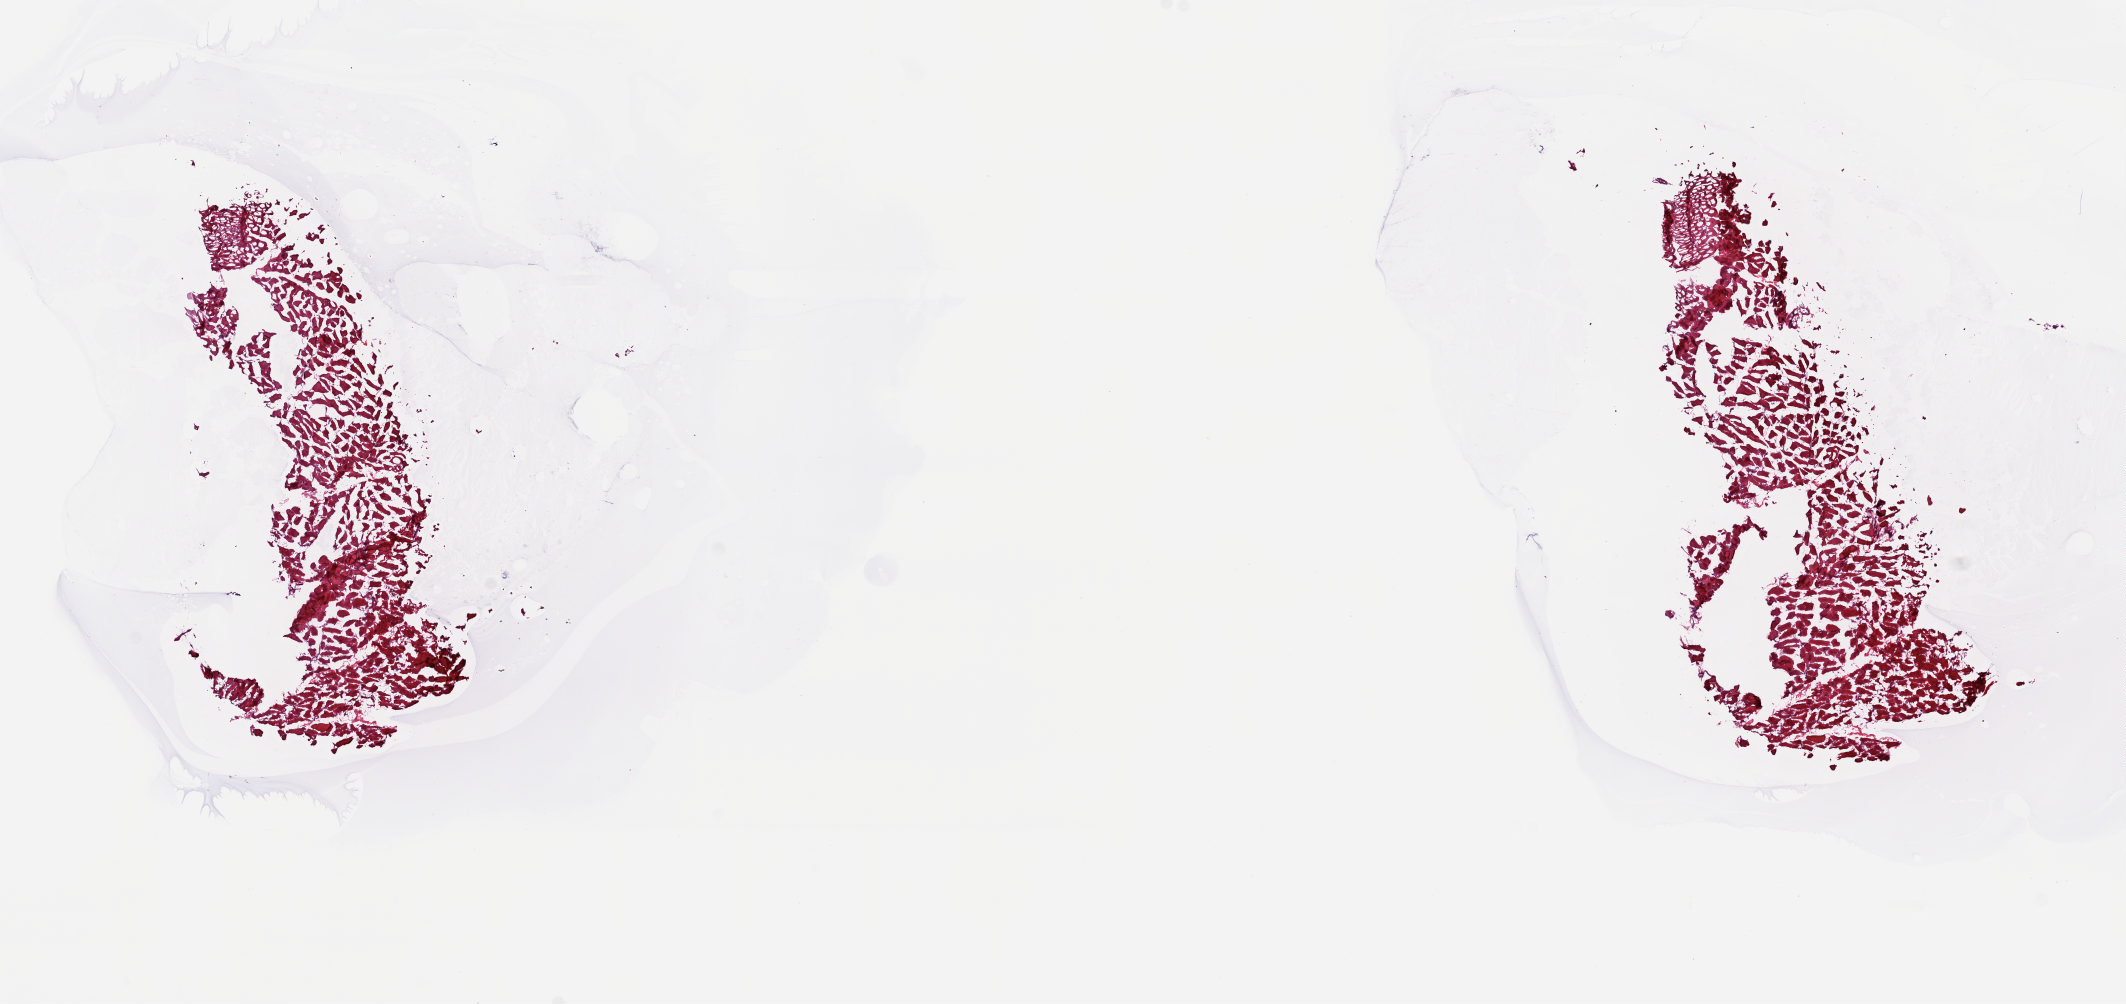
Digitized H&E-stained tissue section (whole slide) — a low-resolution overview of the entire scanned area, about 16.9 x 8.0 mm, frozen section from the top of the tissue portion, sample: solid tissue normal (non-tumour tissue), connective, subcutaneous and other soft tissues. Female patient; age at initial diagnosis 49 years.
This section: solid tissue normal (non-tumour) sample from the same patient. Patient diagnosis: Undifferentiated sarcoma (connective, subcutaneous and other soft tissues of lower limb and hip).